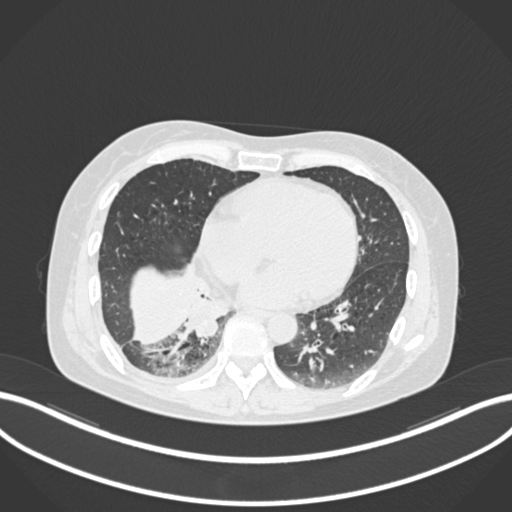
Chest CT, one axial slice; position 55 of 168 along the scan axis; reconstruction kernel B30f; 120 kVp; lung window (W 1500 / L -600 HU); 1 mm slice thickness; 512 × 512 image matrix, field of view 400 × 400 mm. Patient: female, 63 years. Case-level facts recorded for this patient, not image findings: clinical TNM (as recorded): T1c N0 M0.
Structures marked on this image (bounding box drawn by a radiologist):
- lung tumour (recorded histology: adenocarcinoma): bounding box (x1, y1, x2, y2) in pixels: (180, 289, 230, 339)